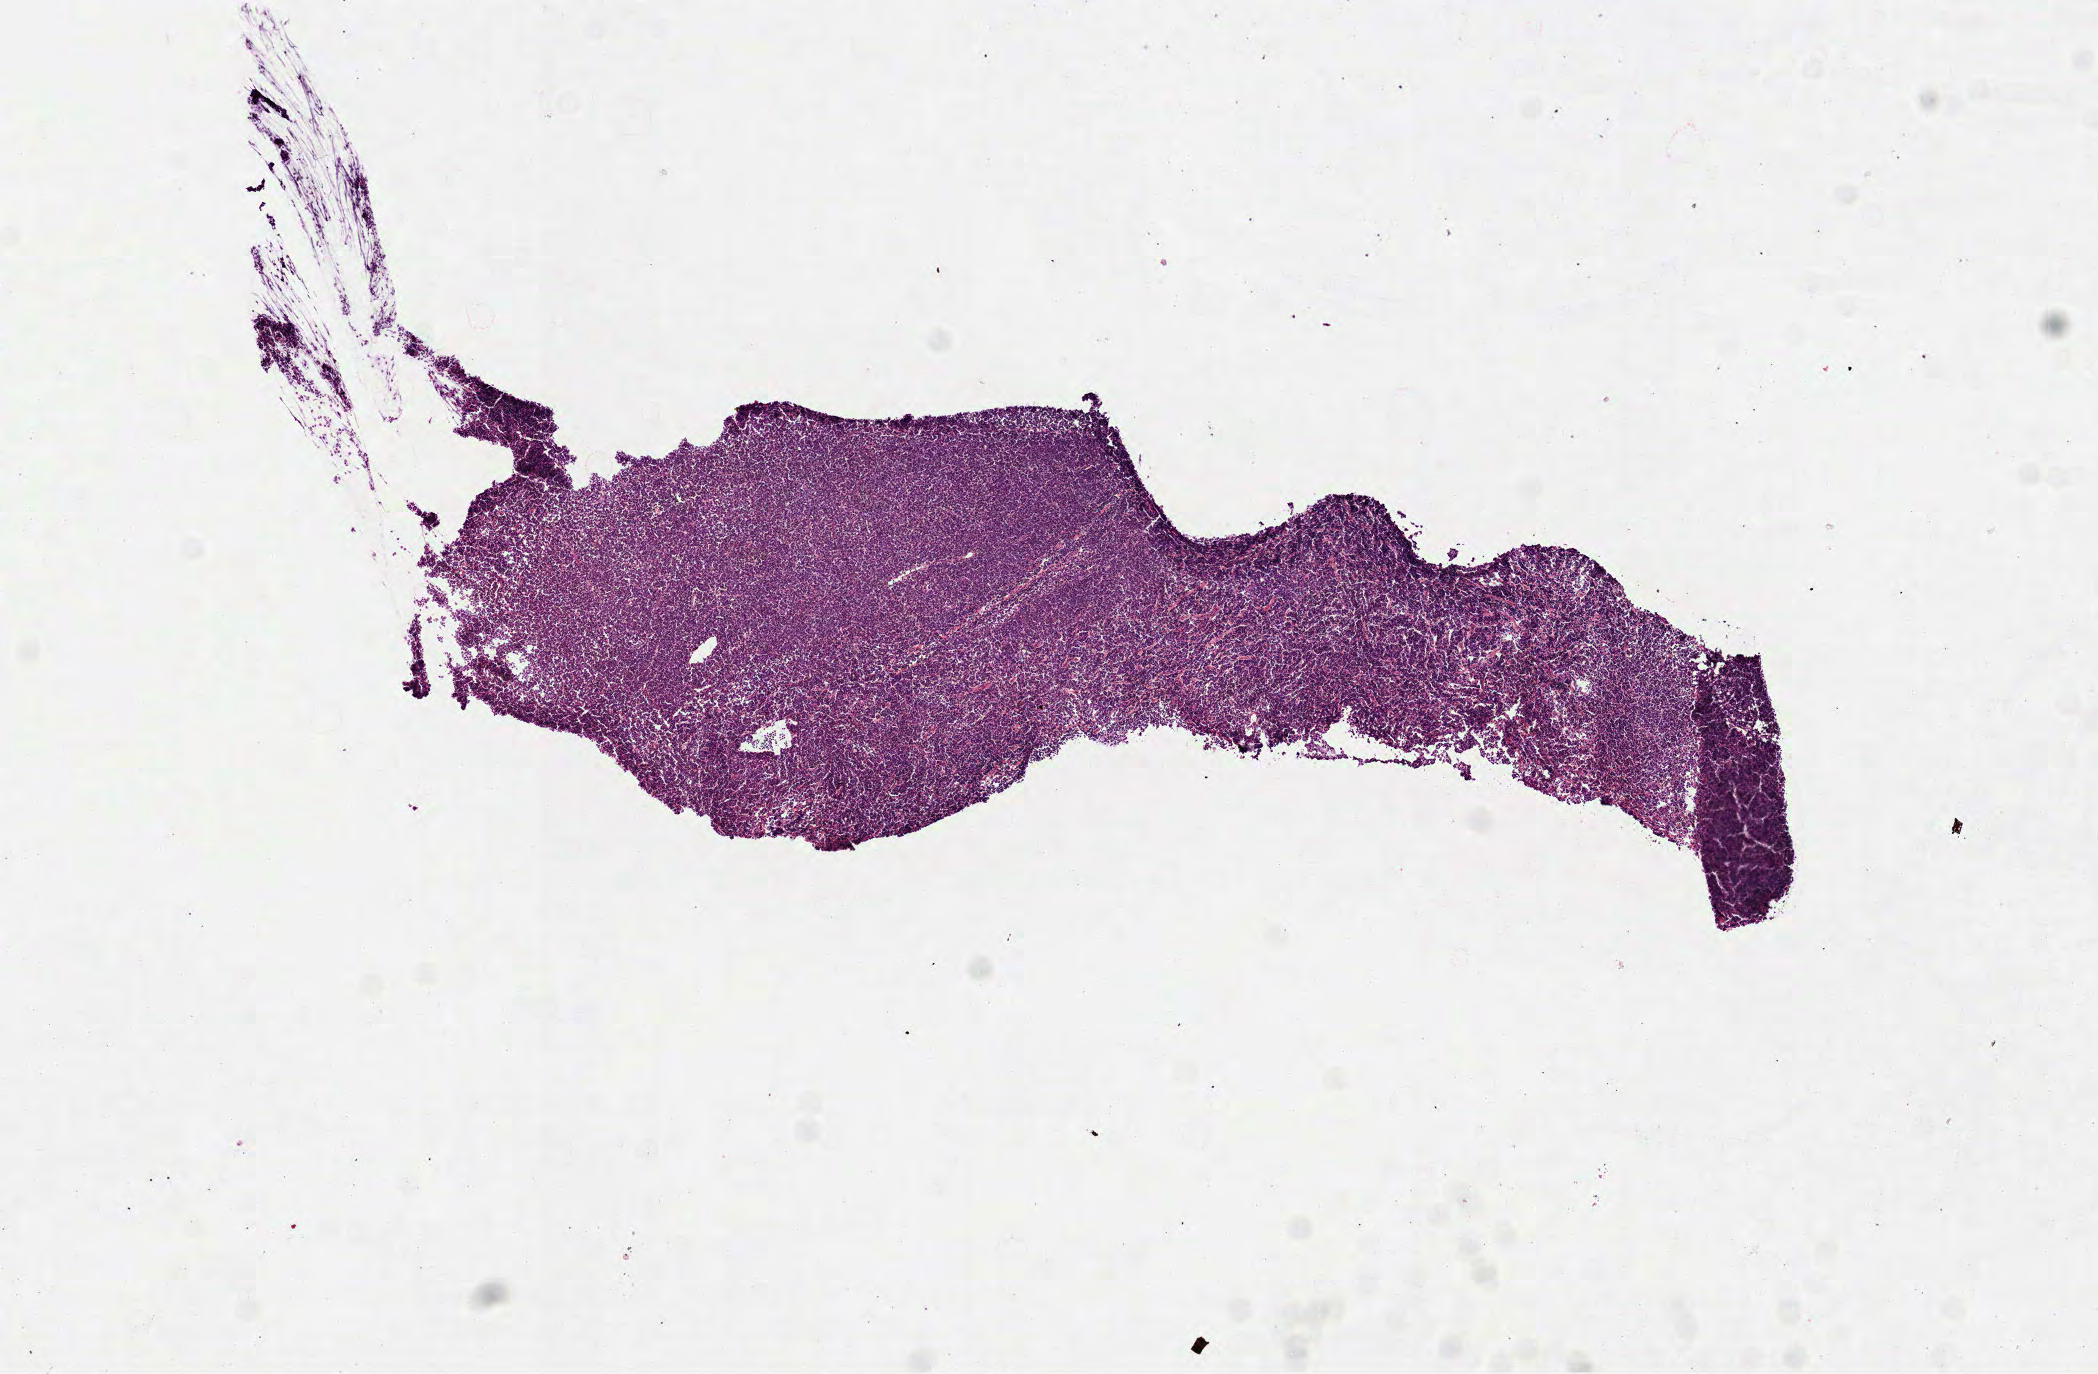
Digitized Hematoxylin and eosin (H&E) stained tissue section (whole slide), a low-resolution overview of the entire scanned area, about 8.5 x 5.5 mm, frozen section from the top of the tissue portion, lymphoid tissue, primary tumour sample. Female patient; age at initial diagnosis 43 years. Slide review estimates, as recorded: tumour cells 95%, tumour nuclei 85%, normal cells 0%, stromal cells 5%, necrosis 0%.
Pathologic diagnosis: Diffuse large B-cell lymphoma, NOS (intra-abdominal lymph nodes).